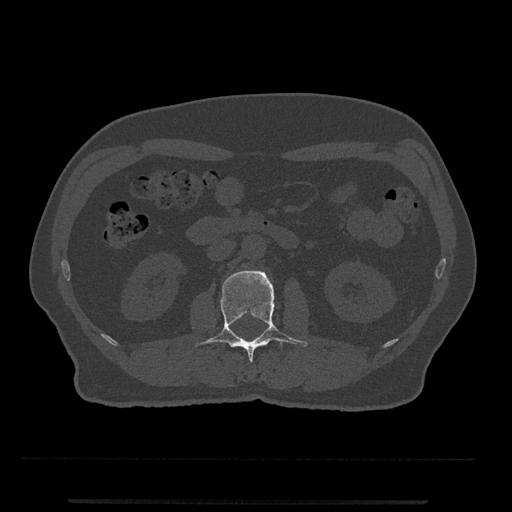
CT including the spine, one axial slice; position 266 of 797 along the scan axis; reconstruction kernel Br40s/3; bone window (W 1800 / L 400 HU); 0.5 mm slice thickness; 512 × 512 image matrix. Male patient, age 63 years. From the clinical record (not read from this slice): primary cancer: prostate.
Annotated regions visible in this slice (semi-automatic segmentation, software-assisted and operator-edited):
- L2 vertebra: bounding box (x1, y1, x2, y2) in pixels: (196, 270, 308, 363)